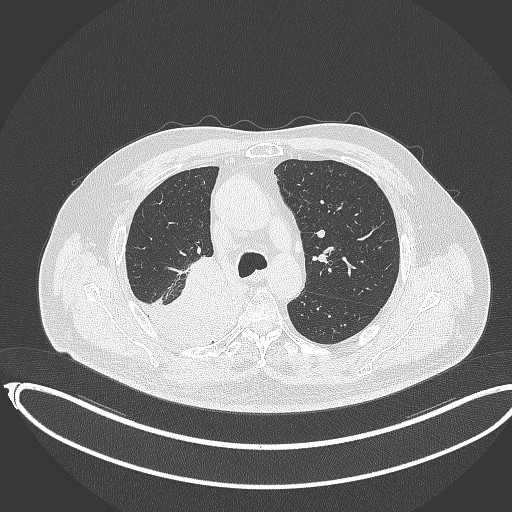
Chest CT, one axial slice; slice 246 of 403 in the series (ordered by position); reconstruction kernel B70f; 120 kVp; lung window (W 1500 / L -600 HU); 1 mm slice thickness; 512 × 512 image matrix, field of view 436 × 436 mm. Male patient, age 68 years. From the clinical record (not read from this slice): clinical TNM (as recorded): T2a N0 M0.
Annotated regions visible in this slice (rectangle marked by the reading radiologist):
- lung tumour (recorded histology: adenocarcinoma): bounding box [x1, y1, x2, y2] px = [121, 258, 246, 356]